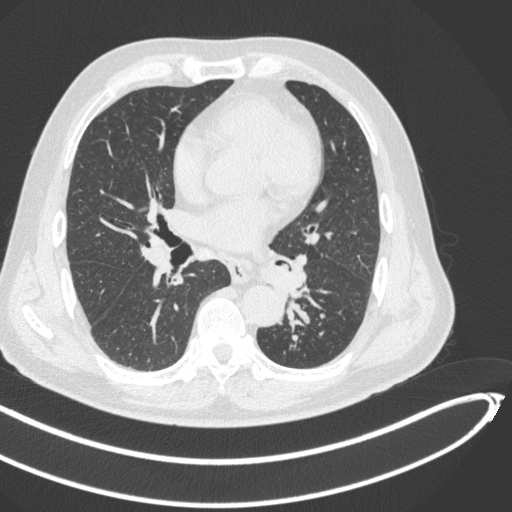
Chest CT, one axial slice; position 238 of 466 along the scan axis; lung window (W 1500 / L -600 HU); 1 mm slice thickness; 512 × 512 image matrix, field of view 400 × 400 mm. Patient: male, 64 years. Case-level facts recorded for this patient, not image findings: clinical TNM (as recorded): T1c N0 M0; histopathological grade: G2.
Structures marked on this image (bounding box drawn by a radiologist):
- lung tumour (recorded histology: squamous cell carcinoma): bounding box <259,253,294,294> (left, top, right, bottom; pixels)